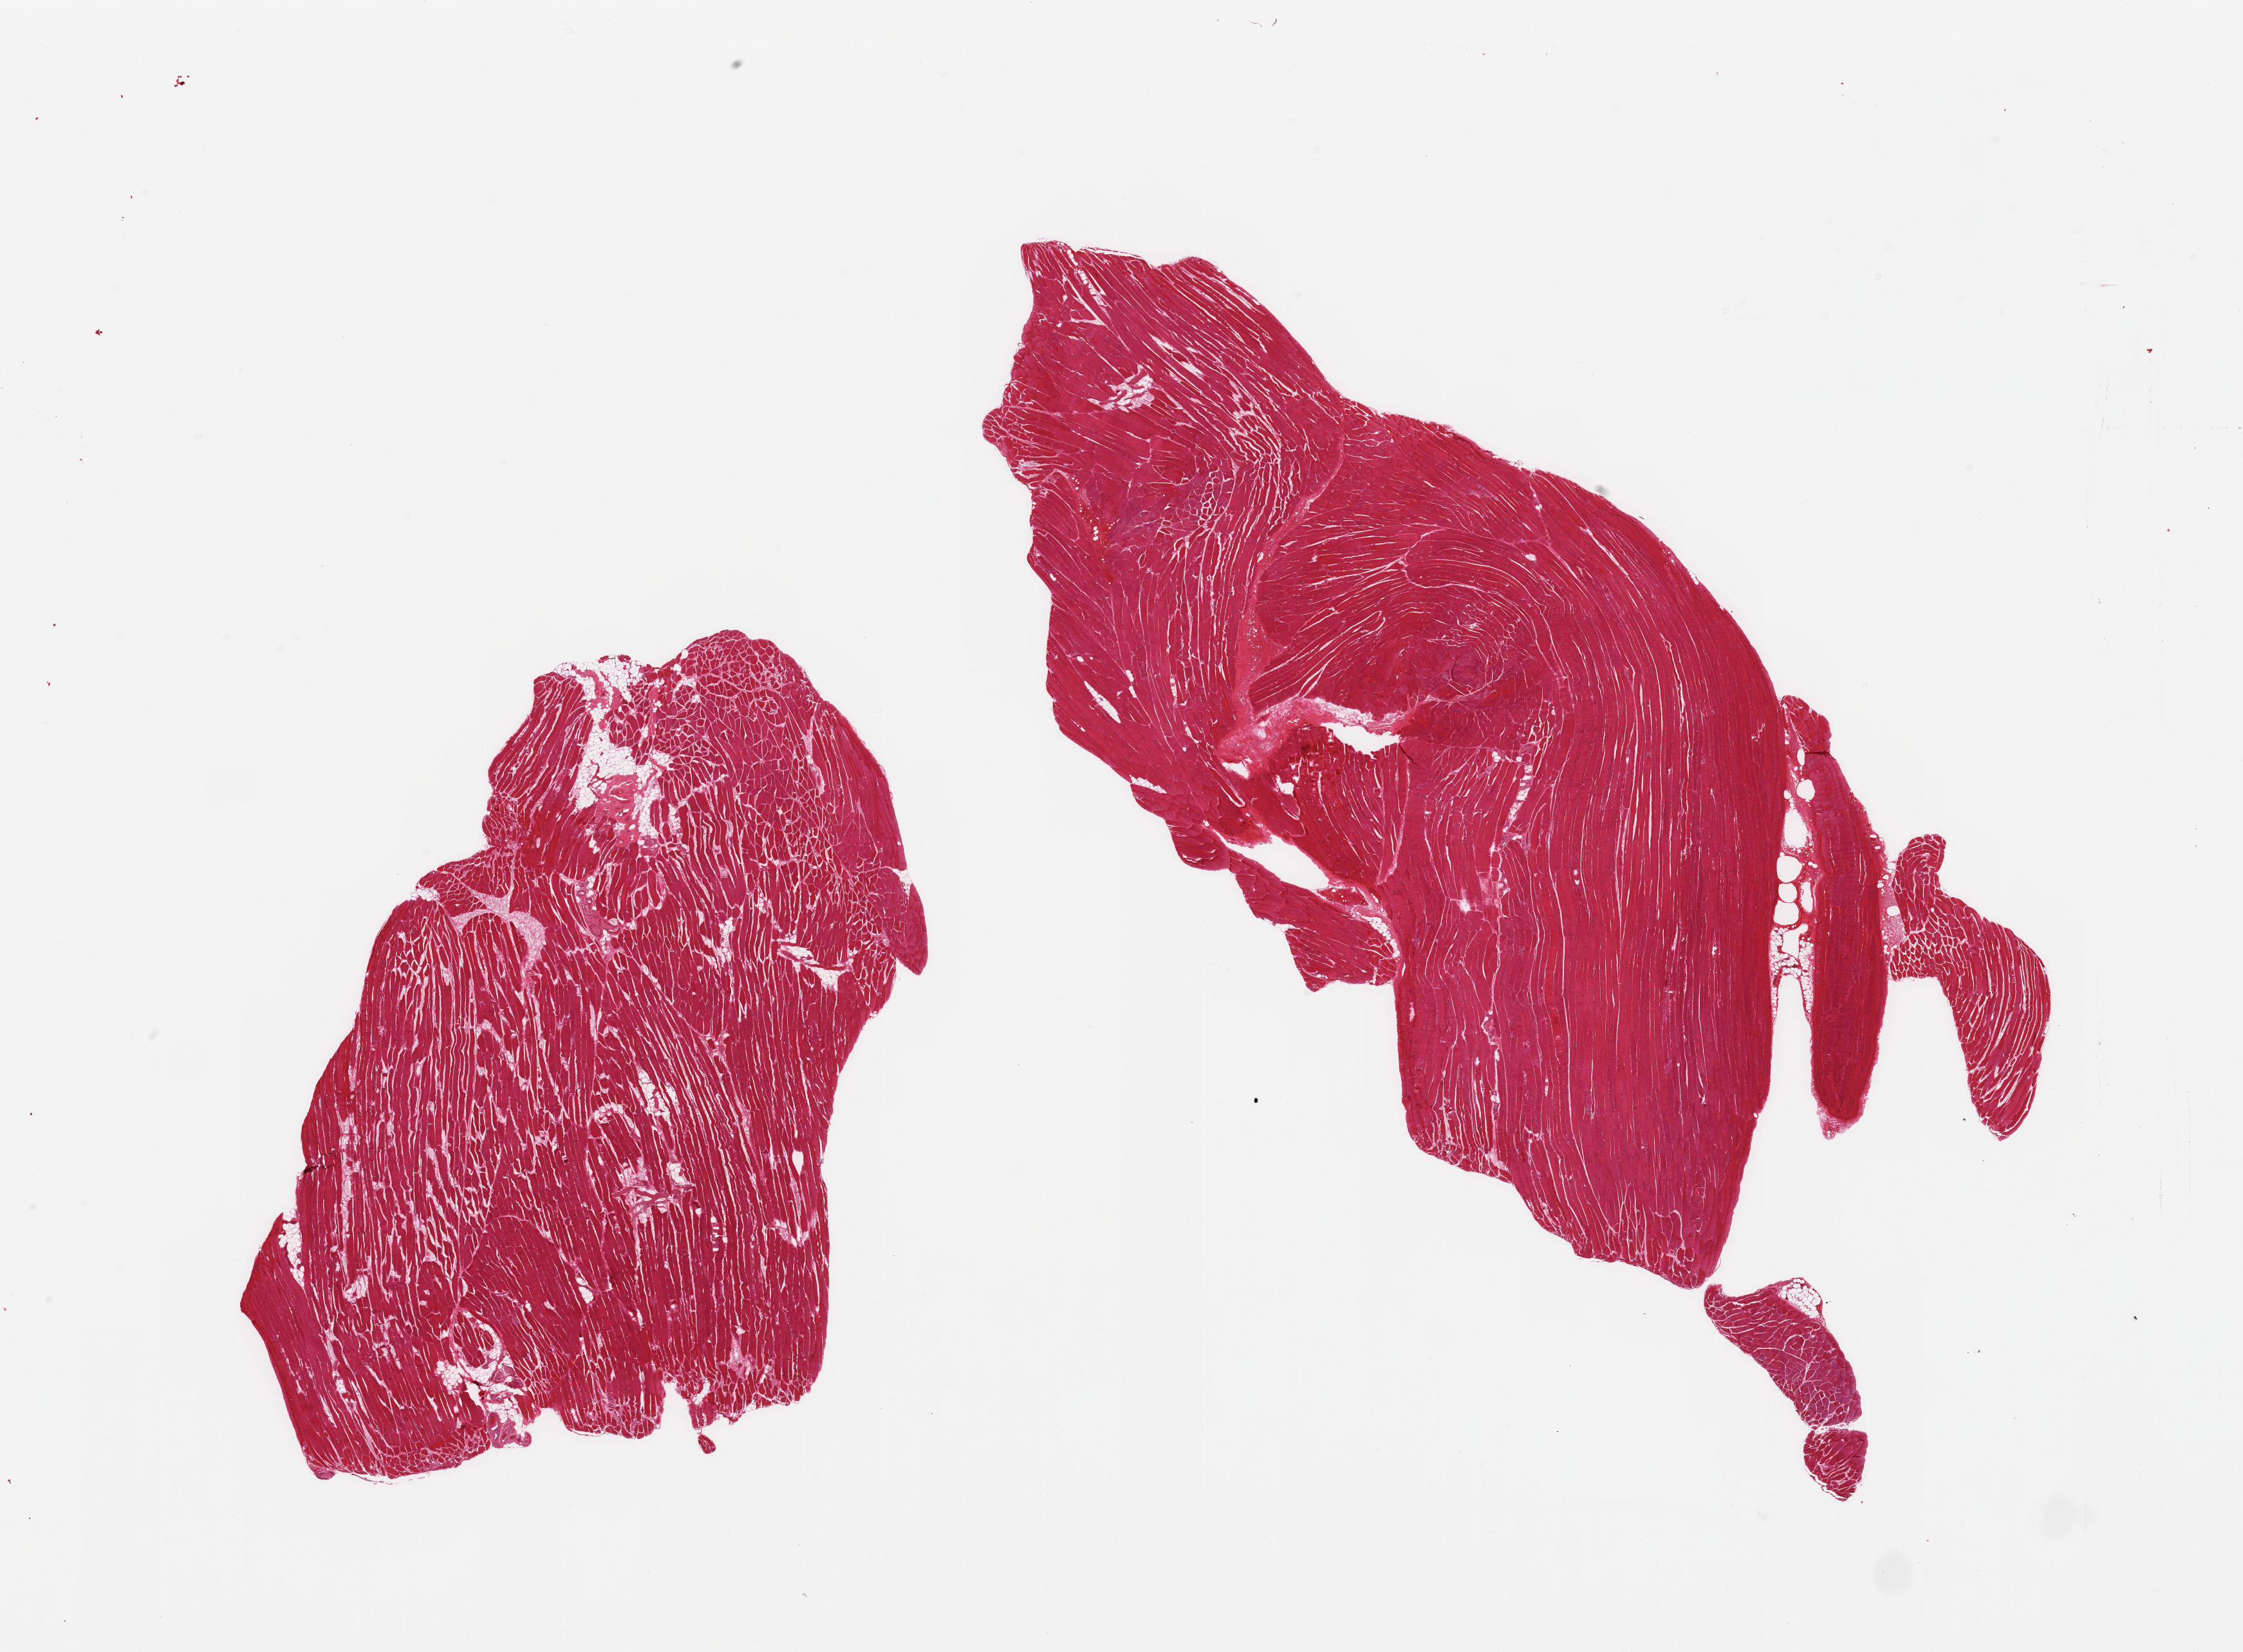
Digitized haematoxylin and eosin-stained section — a low-resolution overview of the entire scanned area, about 27.6 x 20.3 mm (acquisition: 20x scan), PAXgene-fixed paraffin-embedded (PFPE) section, section of skeletal muscle (target tissue), donor tissue sample. Male donor.
* review note (as recorded): 2 pieces; <5% interstitial fat